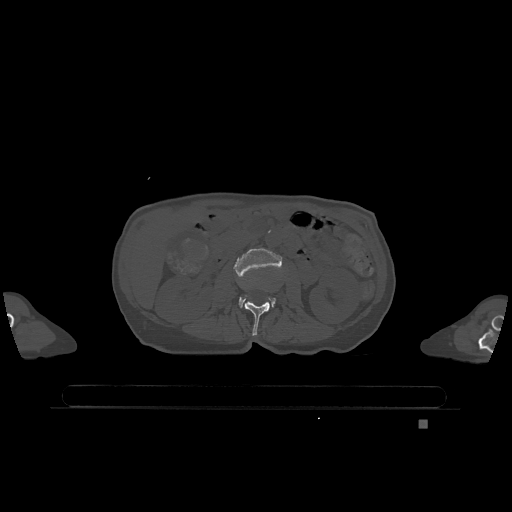
CT including the spine, one axial slice; slice 394 of 1317 in the series (ordered by position); bone window (W 1800 / L 400 HU); 0.5 mm slice thickness; 512 × 512 image matrix, field of view 500 × 500 mm. Patient: female, 74 years. From the clinical record (not read from this slice): primary cancer: lung.
Annotated regions visible in this slice (semi-automatically segmented with operator editing):
- L2 vertebra: bounding box <245,301,270,336> (left, top, right, bottom; pixels)
- L3 vertebra: <234,248,282,308>